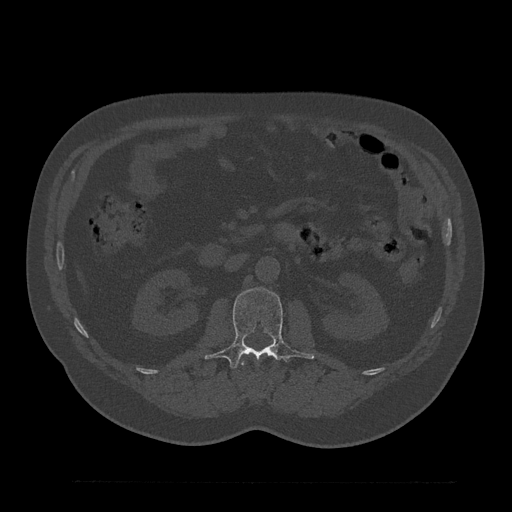
CT including the spine, one axial slice. Position 109 of 797 along the scan axis. 120 kVp. Bone window (W 1800 / L 400 HU). 0.5 mm slice thickness. 512 × 512 image matrix. Male patient, age 61 years. From the clinical record (not read from this slice): primary cancer: prostate.
Structures marked on this image (semi-automatic segmentation, software-assisted and operator-edited):
- L1 vertebra: box from (x=241, y=352) to (x=273, y=365) px
- L2 vertebra: (x=205, y=287)–(x=314, y=370)